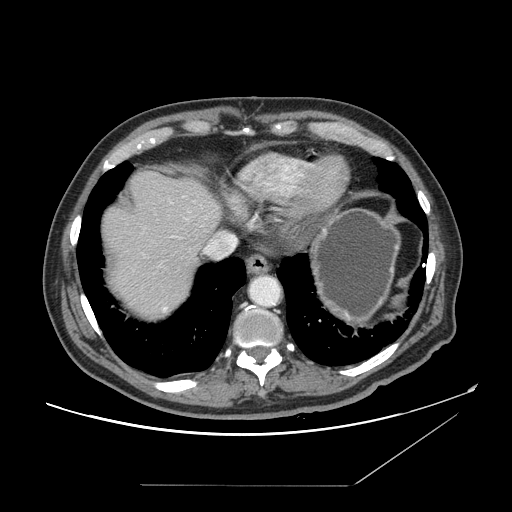
Contrast-enhanced abdominal CT, one axial slice; position 136 of 166 along the scan axis; intravenous contrast given; soft-tissue window (W 400 / L 40 HU); 2.5 mm slice thickness; 512 × 512 image matrix. Male patient, age 80 years. From the clinical record (not read from this slice): diagnosis: colorectal cancer liver metastases, imaged before liver resection; multiple liver metastases: no; largest metastasis: 2.2 cm; chemotherapy before resection: no.
Structures marked on this image (expert manual segmentation):
- hepatic veins: box from (x=180, y=234) to (x=237, y=258) px
- liver: (x=101, y=171)–(x=221, y=320)
- planned liver remnant (the part of the liver to remain after resection): (x=100, y=171)–(x=222, y=259)